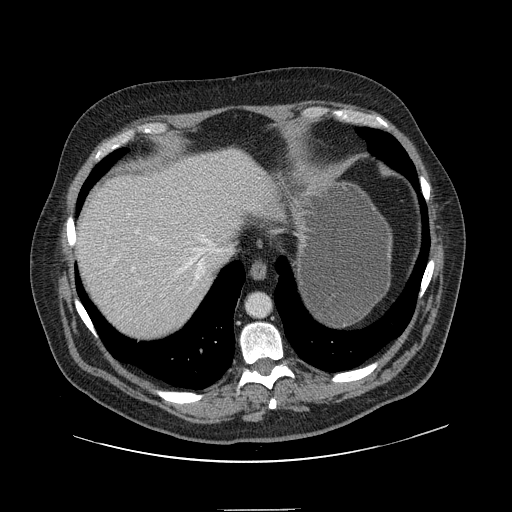
Contrast-enhanced abdominal CT, one axial slice; position 125 of 154 along the scan axis; 120 kVp; intravenous contrast given; soft-tissue window (W 400 / L 40 HU); 2.5 mm slice thickness; 512 × 512 image matrix, field of view 451 × 451 mm. Male patient, age 61 years. From the clinical record (not read from this slice): diagnosis: colorectal cancer liver metastases, imaged before liver resection; multiple liver metastases: yes; largest metastasis: 2.6 cm; disease in both lobes: yes.
Outlined on this slice (expert manual segmentation):
- hepatic veins: bounding box [x1, y1, x2, y2] px = [112, 235, 218, 290]
- liver: [76, 150, 271, 340]
- planned liver remnant (the part of the liver to remain after resection): [76, 150, 271, 341]
- portal vein (with intrahepatic branches): [127, 214, 142, 283]